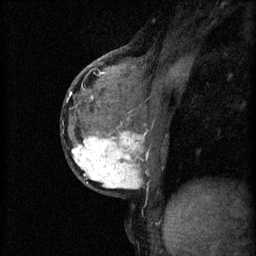
Breast MRI (dynamic contrast-enhanced), one sagittal slice; slice 28 of 60 in the series (ordered by position); 3 images stored at this slice position (order not interpretable as contrast timing); 1.5 T; TE 4.2 ms, TR 11 ms; 256 × 256 image matrix. Female patient, age 37 years.
Annotated regions visible in this slice (semi-automatically segmented with operator editing):
- analysis volume of interest (the breast-tissue region the enhancement analysis was run in; not a lesion): bounding box <68,118,159,195> (left, top, right, bottom; pixels)
- tumour enhancement mask (voxels above the 70 % enhancement threshold inside the analysis volume of interest): <72,128,148,189>